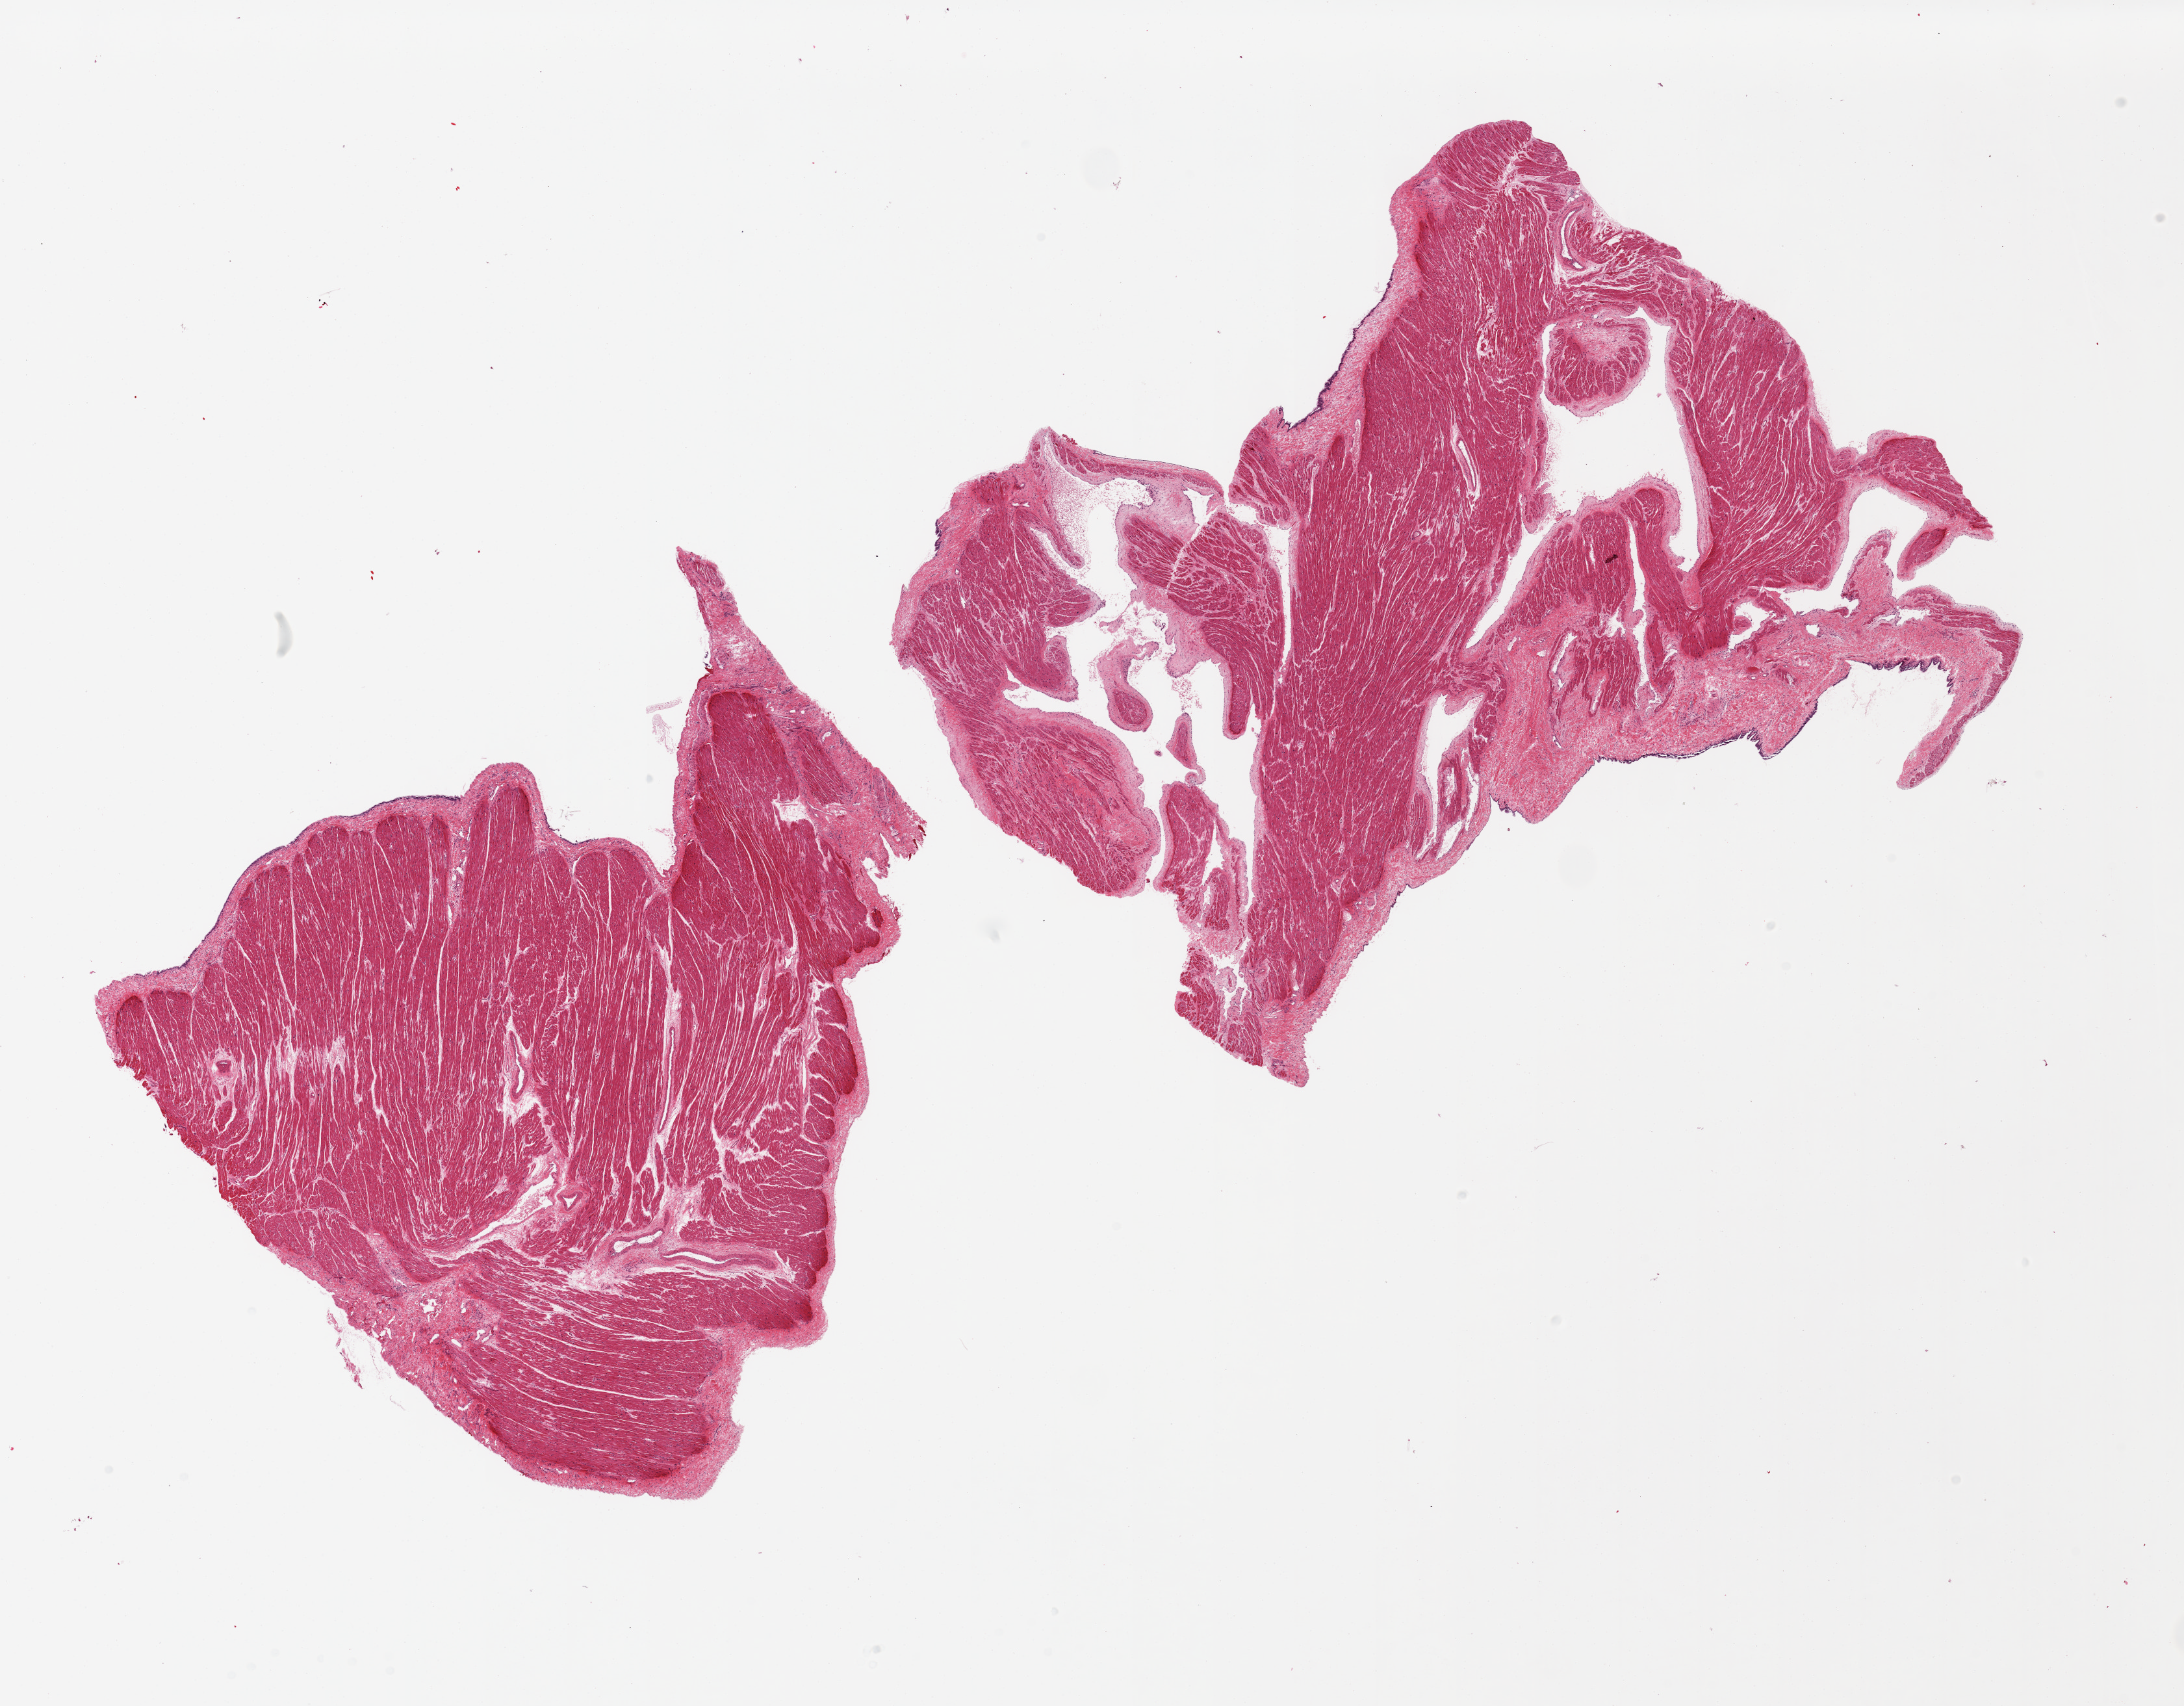
Digitized haematoxylin and eosin-stained section, low-resolution overview of the scanned area, about 26.6 x 20.8 mm. PAXgene-fixed, paraffin-embedded tissue. Target tissue: auricular appendage. Donor tissue sample.
Pathologist's review note for this sample: 2 pieces.